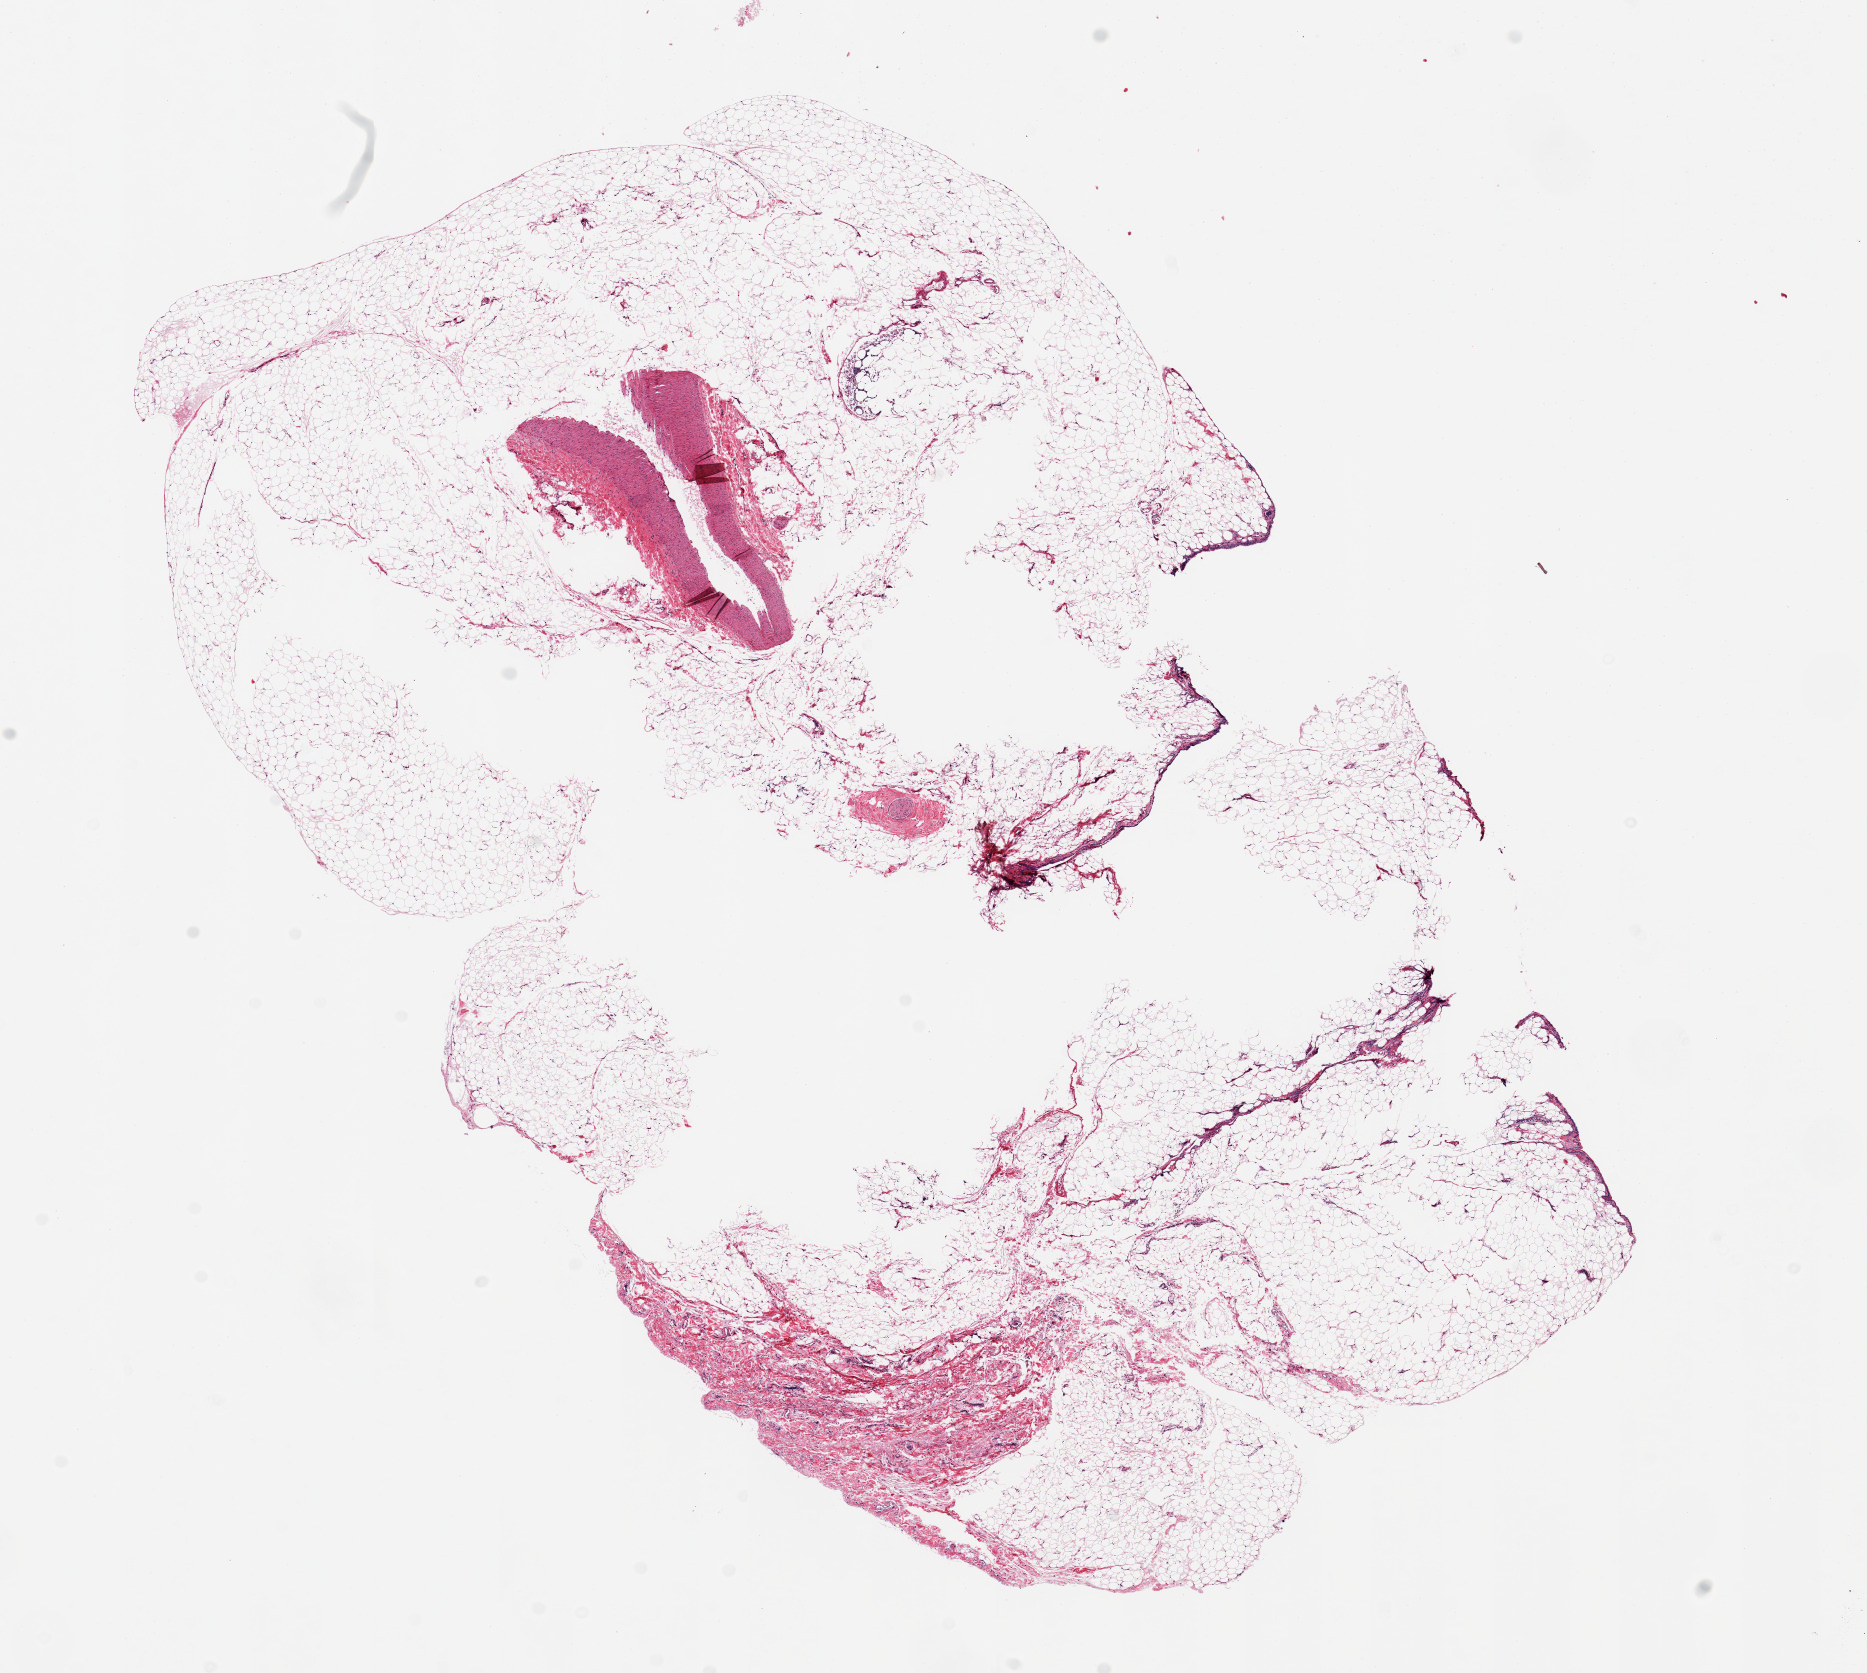
Whole-slide image, haematoxylin and eosin stain, shown as a low-resolution overview of the whole scanned area (about 14.8 x 13.2 mm). PAXgene-fixed paraffin-embedded (PFPE) section. Target tissue: omentum. Tissue donor sample. Donor: male.
Pathologist's review note for this sample: 1 piece ~12x8mm.